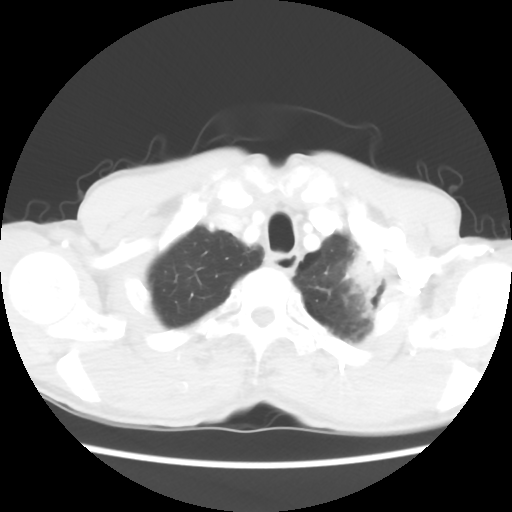
Chest CT, one axial slice; position 54 of 60 along the scan axis; reconstruction kernel STANDARD; 120 kVp; lung window (W 1500 / L -600 HU); 5 mm slice thickness; 512 × 512 image matrix, field of view 308 × 308 mm. Patient: male, 64 years. Case-level facts recorded for this patient, not image findings: clinical TNM (as recorded): T3 N3 M0; histopathological grade: G3.
Outlined on this slice (rectangle marked by the reading radiologist):
- lung tumour (recorded histology: adenocarcinoma): bounding box <342,238,398,324> (left, top, right, bottom; pixels)